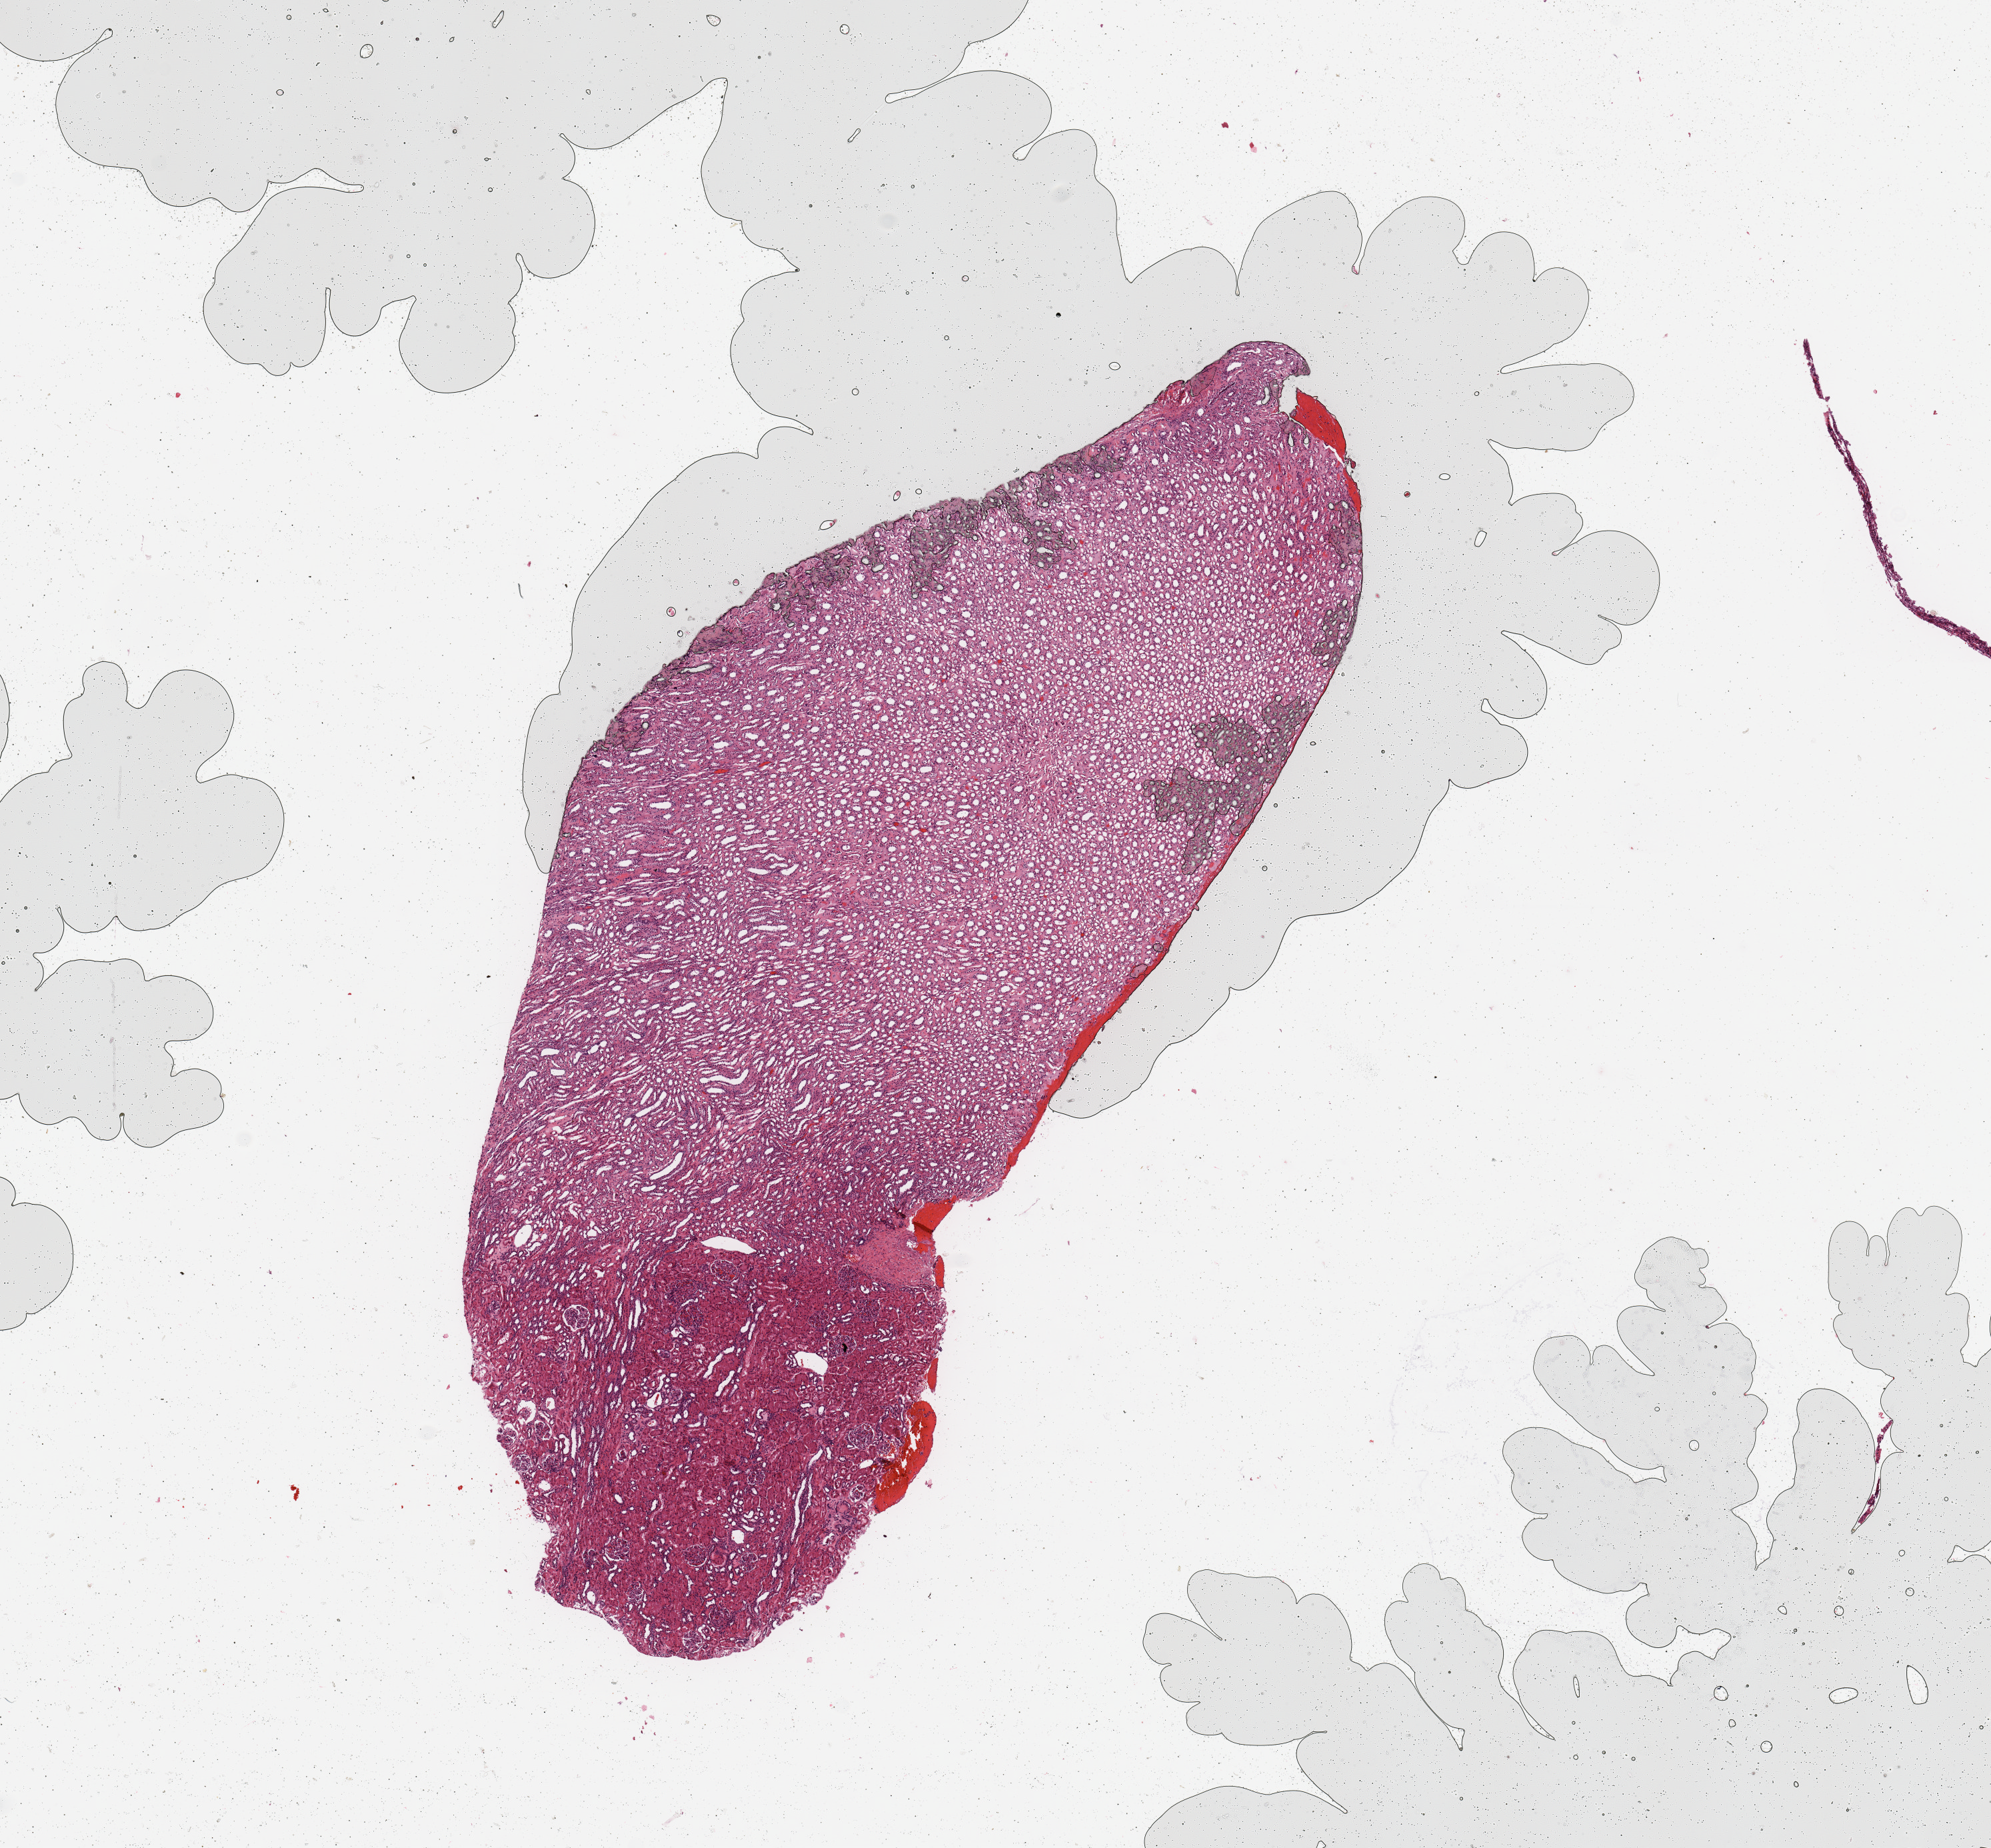
Whole-slide histology image, Hematoxylin and eosin (H&E) stained — whole scanned area (about 11.8 x 11.0 mm, from a 20x scan) shown as a low-resolution overview; normal (non-tumour) tissue sample, kidney. Patient: female, age 57 years.
This section: normal (non-tumour) tissue from the same patient. Patient diagnosis: Renal cell carcinoma, NOS.